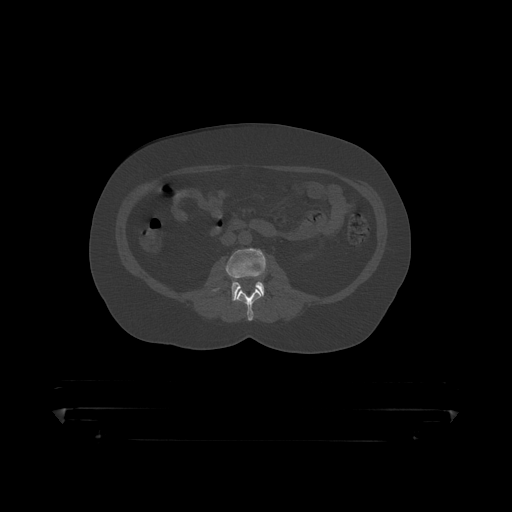
CT including the spine, one axial slice. Slice 103 of 390 in the series (ordered by position). Reconstruction kernel STANDARD. 120 kVp. Bone window (W 1800 / L 400 HU). 512 × 512 image matrix. Male patient, age 60 years. Case-level facts recorded for this patient, not image findings: primary cancer: prostate.
Annotated regions visible in this slice (semi-automatic segmentation, software-assisted and operator-edited):
- L2 vertebra: bounding box <237,288,263,319> (left, top, right, bottom; pixels)
- L3 vertebra: <214,248,266,301>